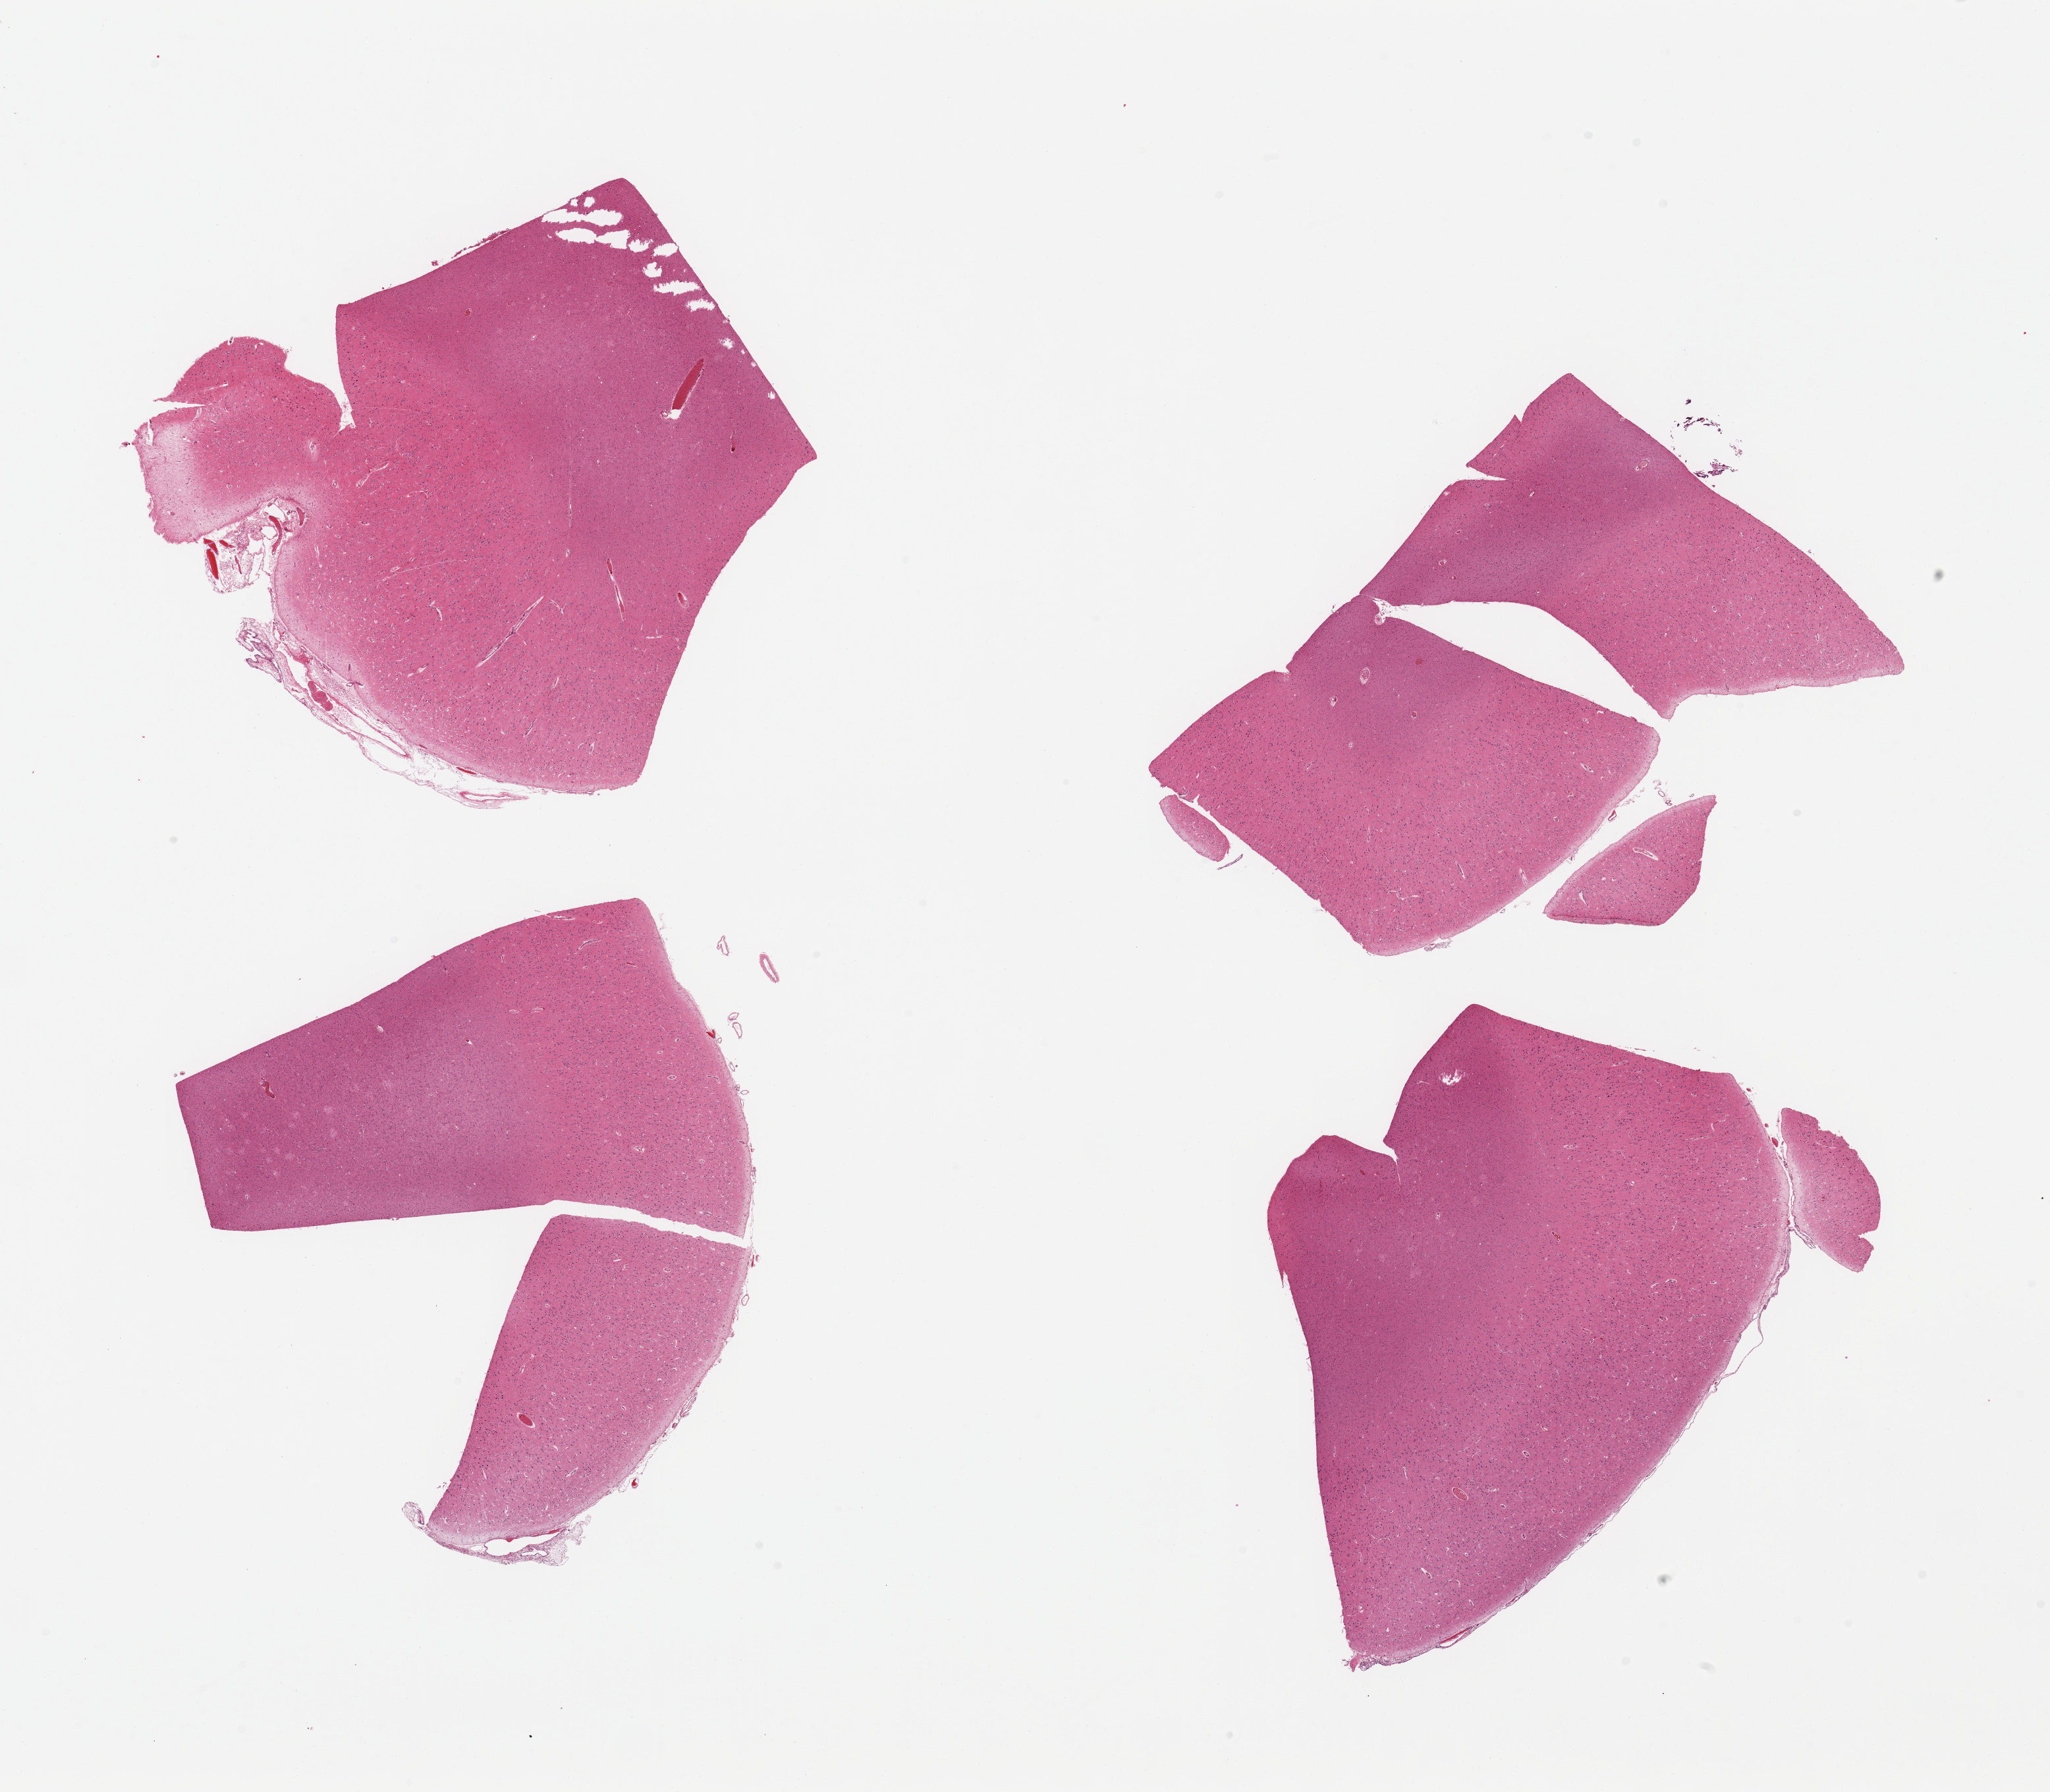
H&E whole-slide image — whole scanned area (about 24.6 x 21.5 mm) shown as a low-resolution overview; PAXgene-fixed, paraffin-embedded tissue; section of cerebral cortex (target tissue); tissue donor sample. Donor sex: male.
Pathologist's review note for this sample: 4 pieces; adherent meninges on 1 piece.